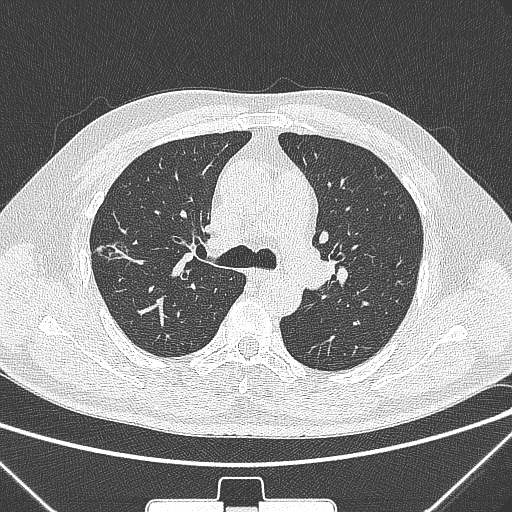
Chest CT, one axial slice; slice 201 of 320 in the series (ordered by position); 120 kVp; lung window (W 1500 / L -600 HU); 512 × 512 image matrix, field of view 350 × 350 mm. Patient: male, 58 years. Case-level facts recorded for this patient, not image findings: clinical TNM (as recorded): T1c N0 M0; histopathological grade: G2.
Structures marked on this image (bounding box drawn by a radiologist):
- lung tumour (recorded histology: adenocarcinoma): box from (x=95, y=236) to (x=131, y=264) px